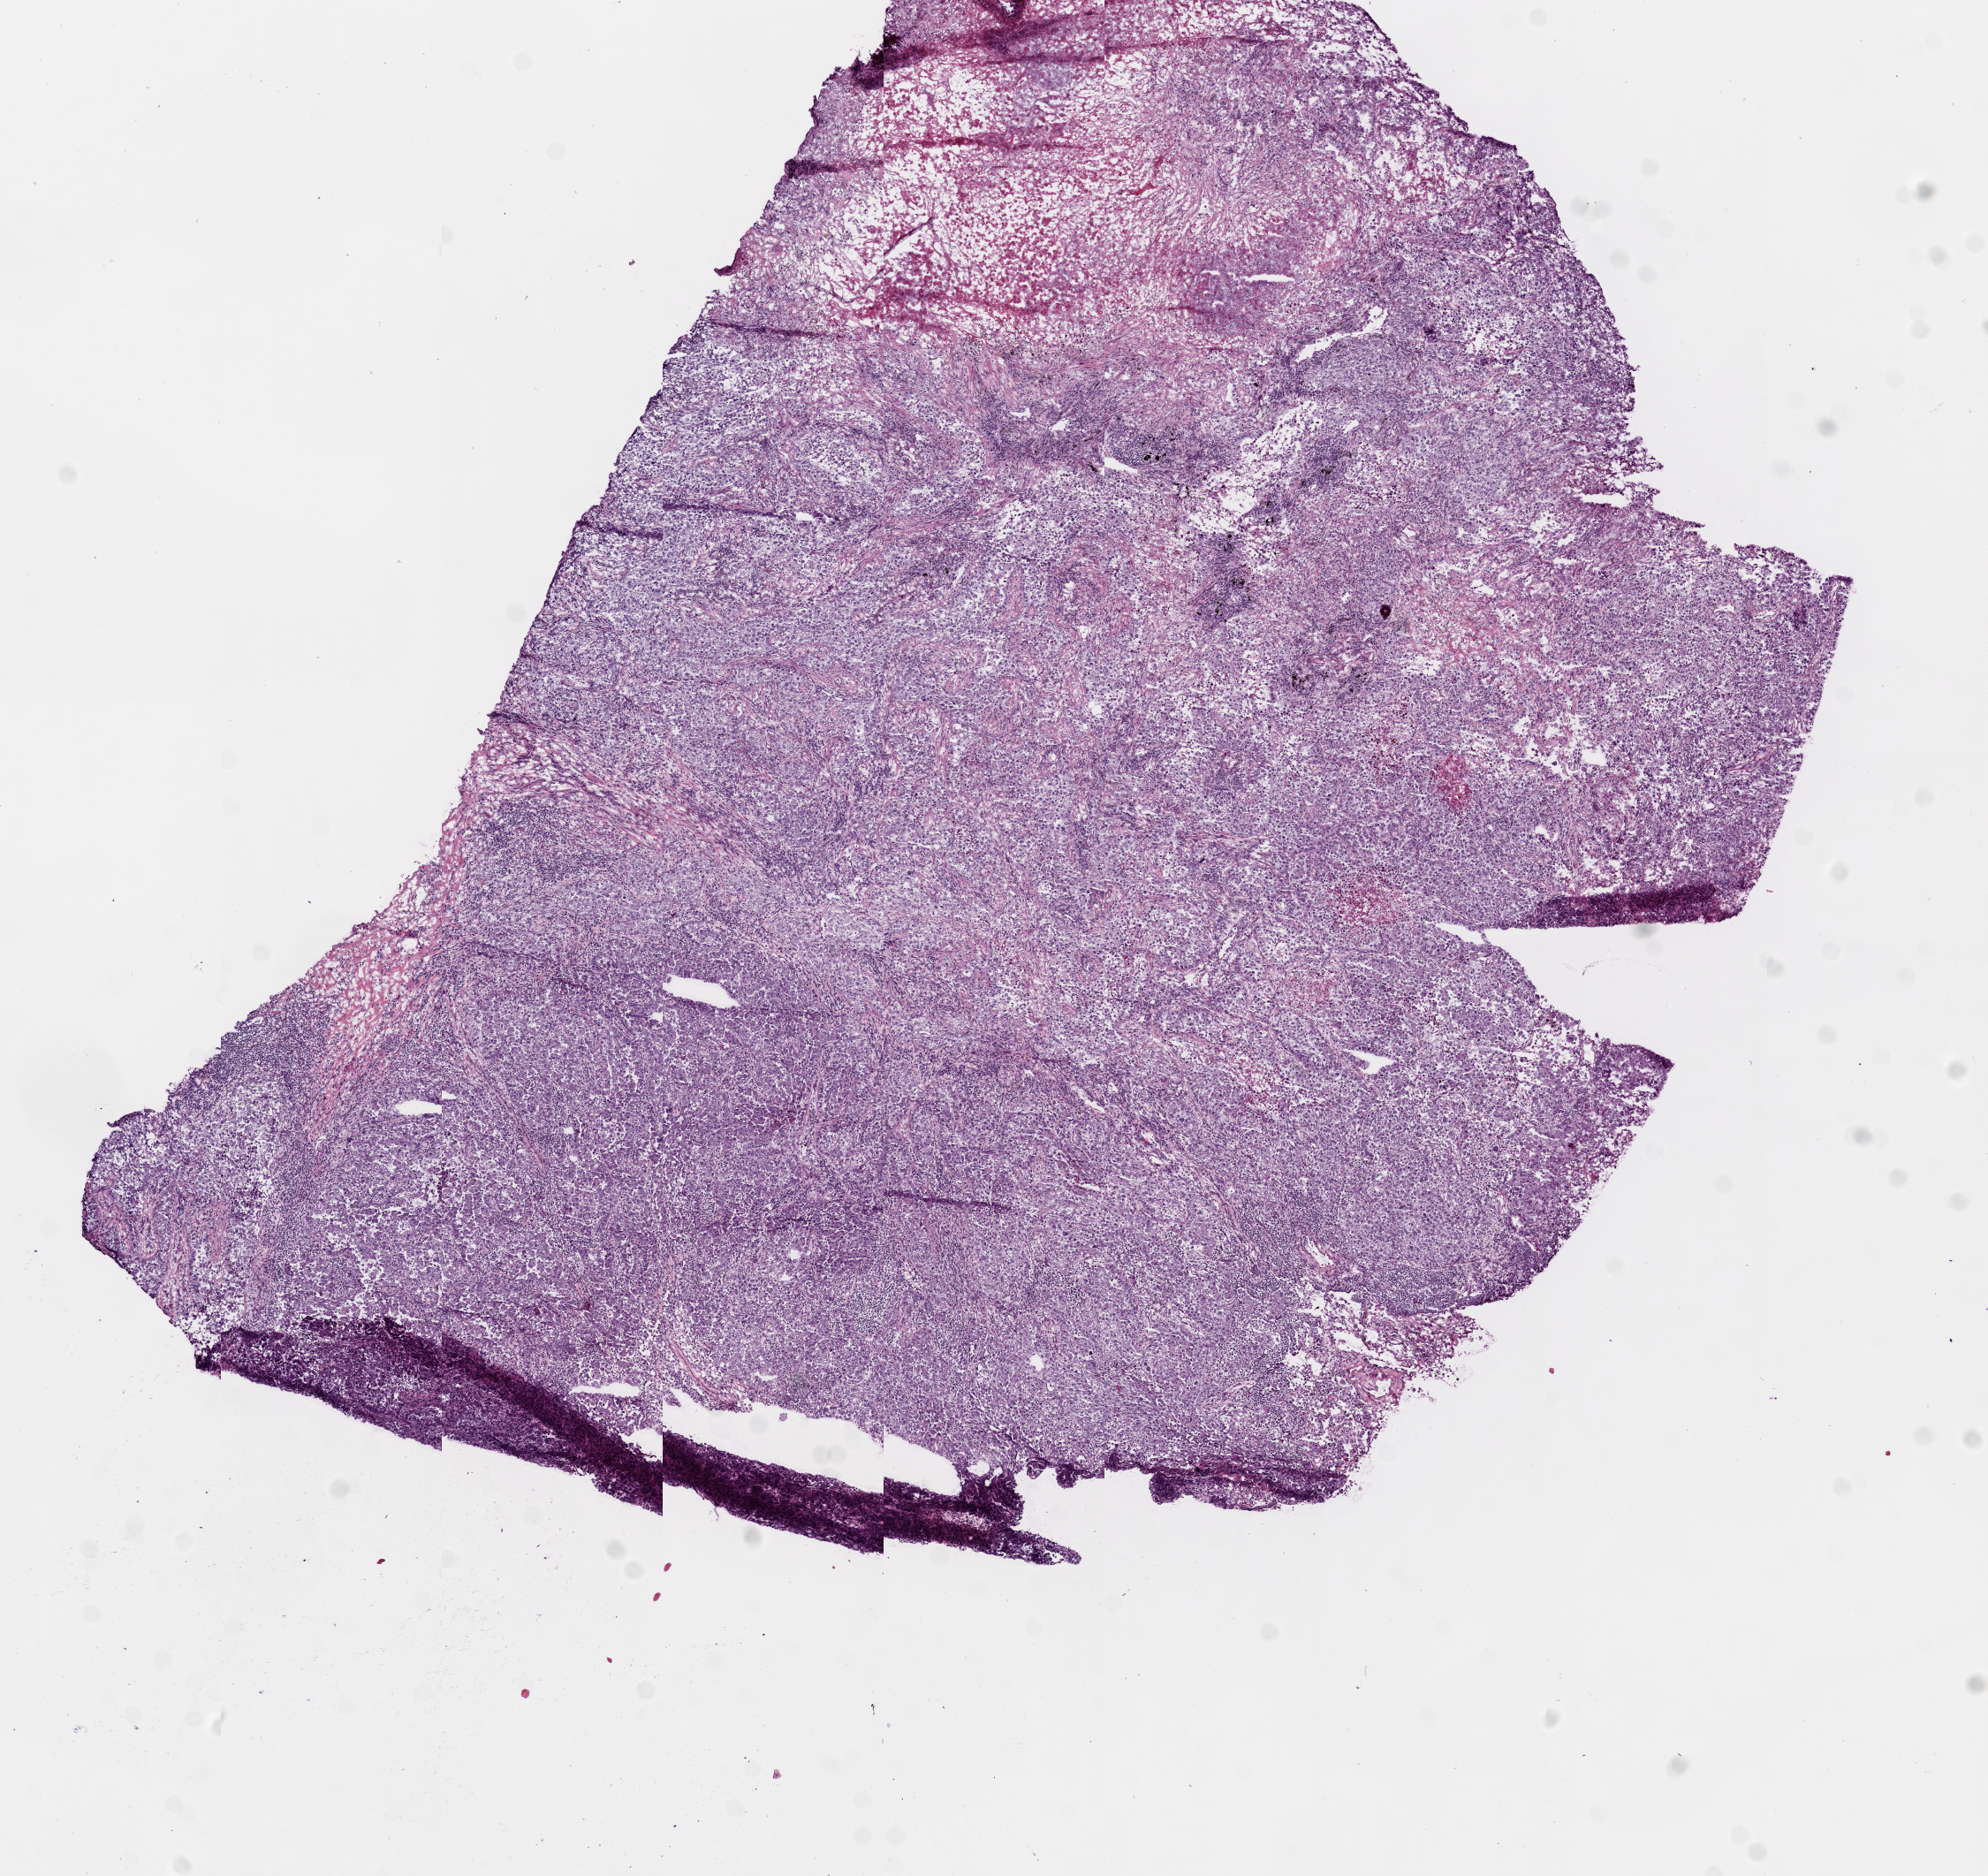
Whole-slide histology image, Hematoxylin and eosin (H&E) stained — a low-resolution overview of the entire scanned area, about 9.0 x 8.5 mm (slide scanned at 20x), frozen section from the top of the tissue portion, primary tumour sample from the lung. Female patient; age at initial diagnosis 47 years.
Histologic diagnosis: Adenocarcinoma with mixed subtypes (upper lobe, lung).